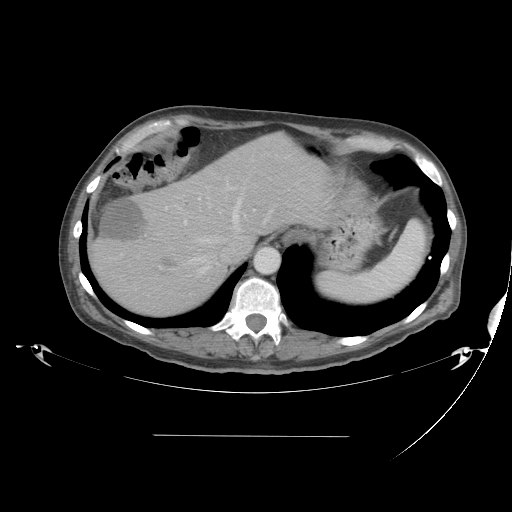
Contrast-enhanced abdominal CT, one axial slice; position 34 of 48 along the scan axis; reconstruction kernel STANDARD; intravenous contrast given; soft-tissue window (W 400 / L 40 HU); 5 mm slice thickness; 512 × 512 image matrix. Male patient, age 65 years. Case-level facts recorded for this patient, not image findings: diagnosis: colorectal cancer liver metastases, imaged before liver resection; multiple liver metastases: yes; largest metastasis: 11 cm.
Annotated regions visible in this slice (outlined manually by an expert reader):
- hepatic veins: bounding box (x1, y1, x2, y2) in pixels: (173, 160, 270, 277)
- liver: (90, 134, 329, 317)
- planned liver remnant (the part of the liver to remain after resection): (174, 134, 330, 238)
- portal vein (with intrahepatic branches): (170, 181, 256, 226)
- liver metastasis: (159, 254, 172, 267)
- liver metastasis: (100, 199, 143, 240)